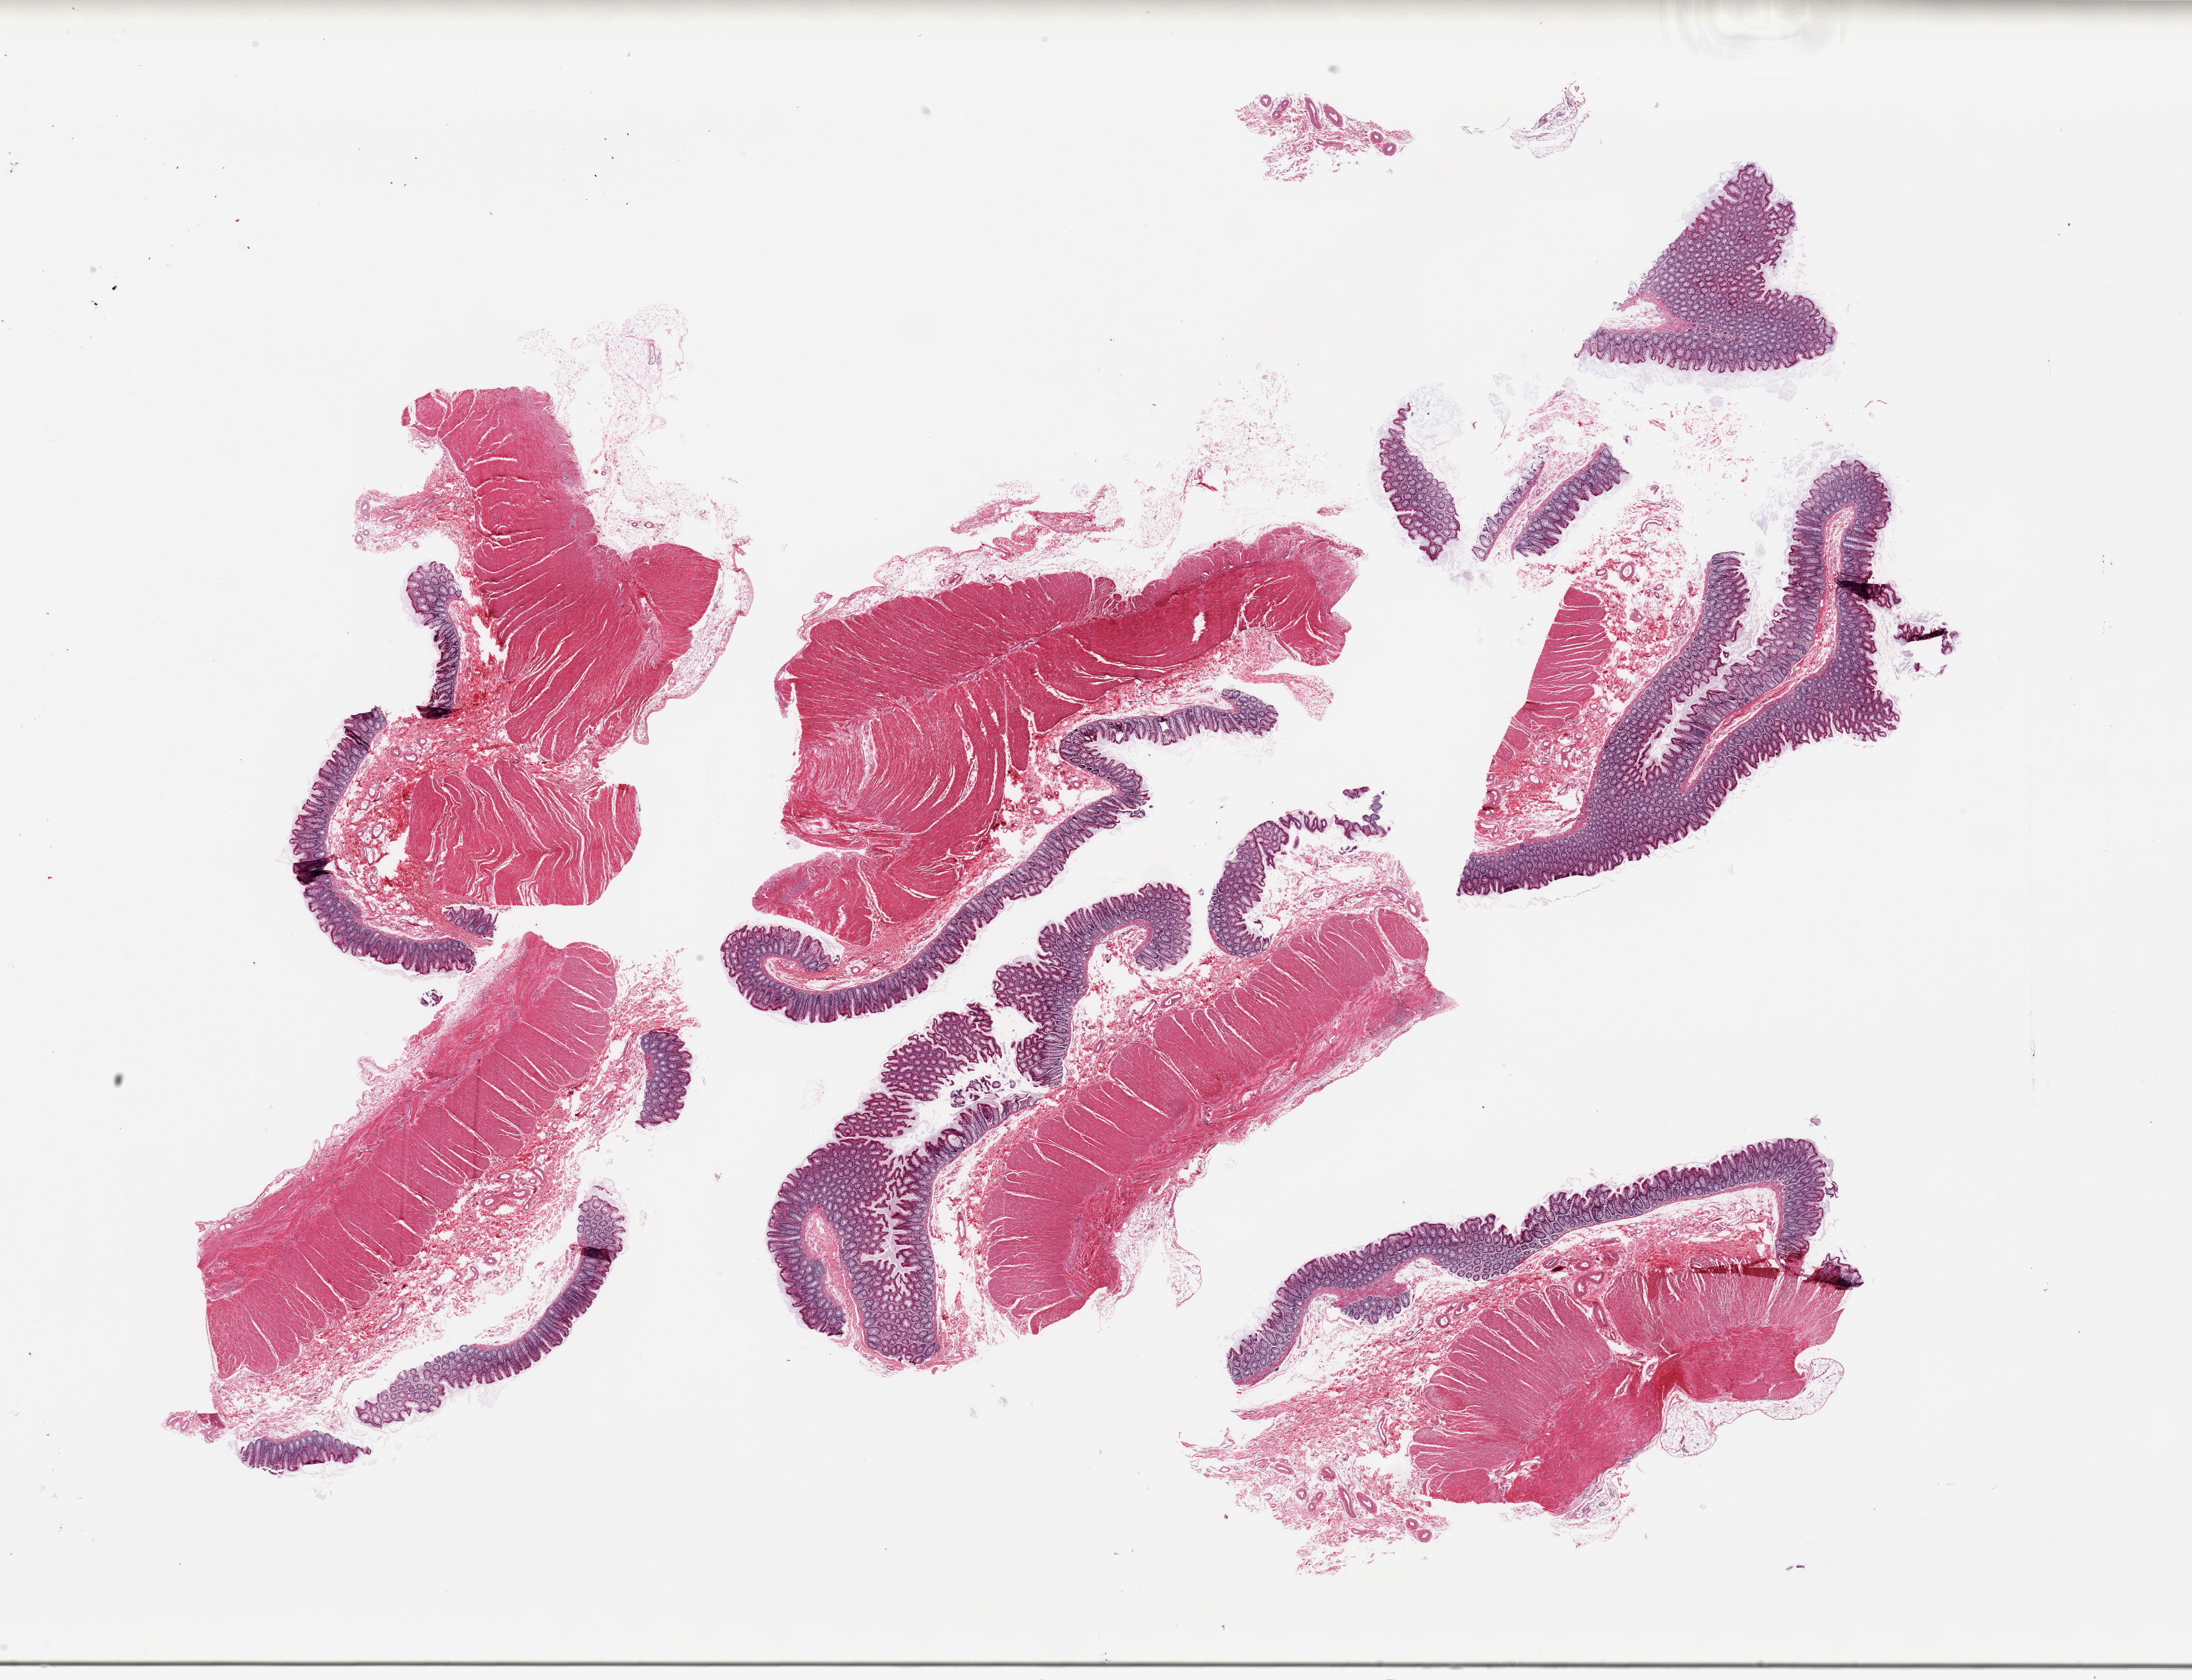
Hematoxylin and eosin (H&E) whole-slide image — low-resolution overview of the scanned area, about 30.5 x 23.4 mm, PAXgene-fixed, paraffin-embedded tissue, sampled site (target tissue): sigmoid colon, tissue donor sample. Male donor.
• review note (as recorded): 6 pieces, ~30% 'contaminant mucosa; rest is target muscularis